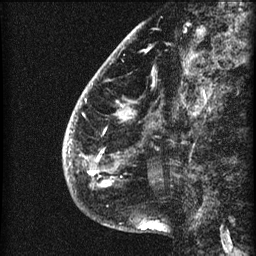
Breast MRI (dynamic contrast-enhanced), one sagittal slice; slice 16 of 60 in the series (ordered by position); 3 images stored at this slice position (order not interpretable as contrast timing); 1.5 T; TE 4.2 ms, TR 22.7 ms; 2 mm slice thickness; 256 × 256 image matrix, field of view 180 × 180 mm. Patient: female, 48 years. Case-level facts recorded for this patient, not image findings: setting: breast cancer imaged before/during neoadjuvant chemotherapy; receptor status: triple-negative.
Structures marked on this image (semi-automatically segmented with operator editing):
- analysis volume of interest (the breast-tissue region the enhancement analysis was run in; not a lesion): bounding box <63,30,173,207> (left, top, right, bottom; pixels)
- tumour enhancement mask (voxels above the 90 % enhancement threshold inside the analysis volume of interest): <64,104,123,188>